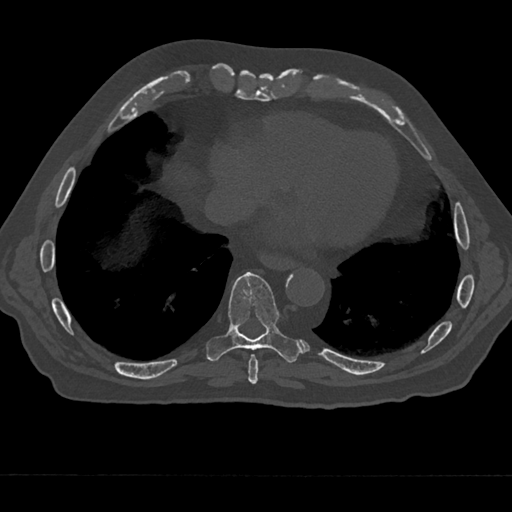
CT including the spine, one axial slice. Slice 269 of 797 in the series (ordered by position). Reconstruction kernel Br40s/3. 120 kVp. Bone window (W 1800 / L 400 HU). 0.5 mm slice thickness. 512 × 512 image matrix, field of view 377 × 377 mm. Male patient, age 75 years. From the clinical record (not read from this slice): primary cancer: renal.
Annotated regions visible in this slice (semi-automatically segmented with operator editing):
- T8 vertebra: bounding box (x1, y1, x2, y2) in pixels: (248, 354, 258, 385)
- T9 vertebra: (206, 272, 301, 362)